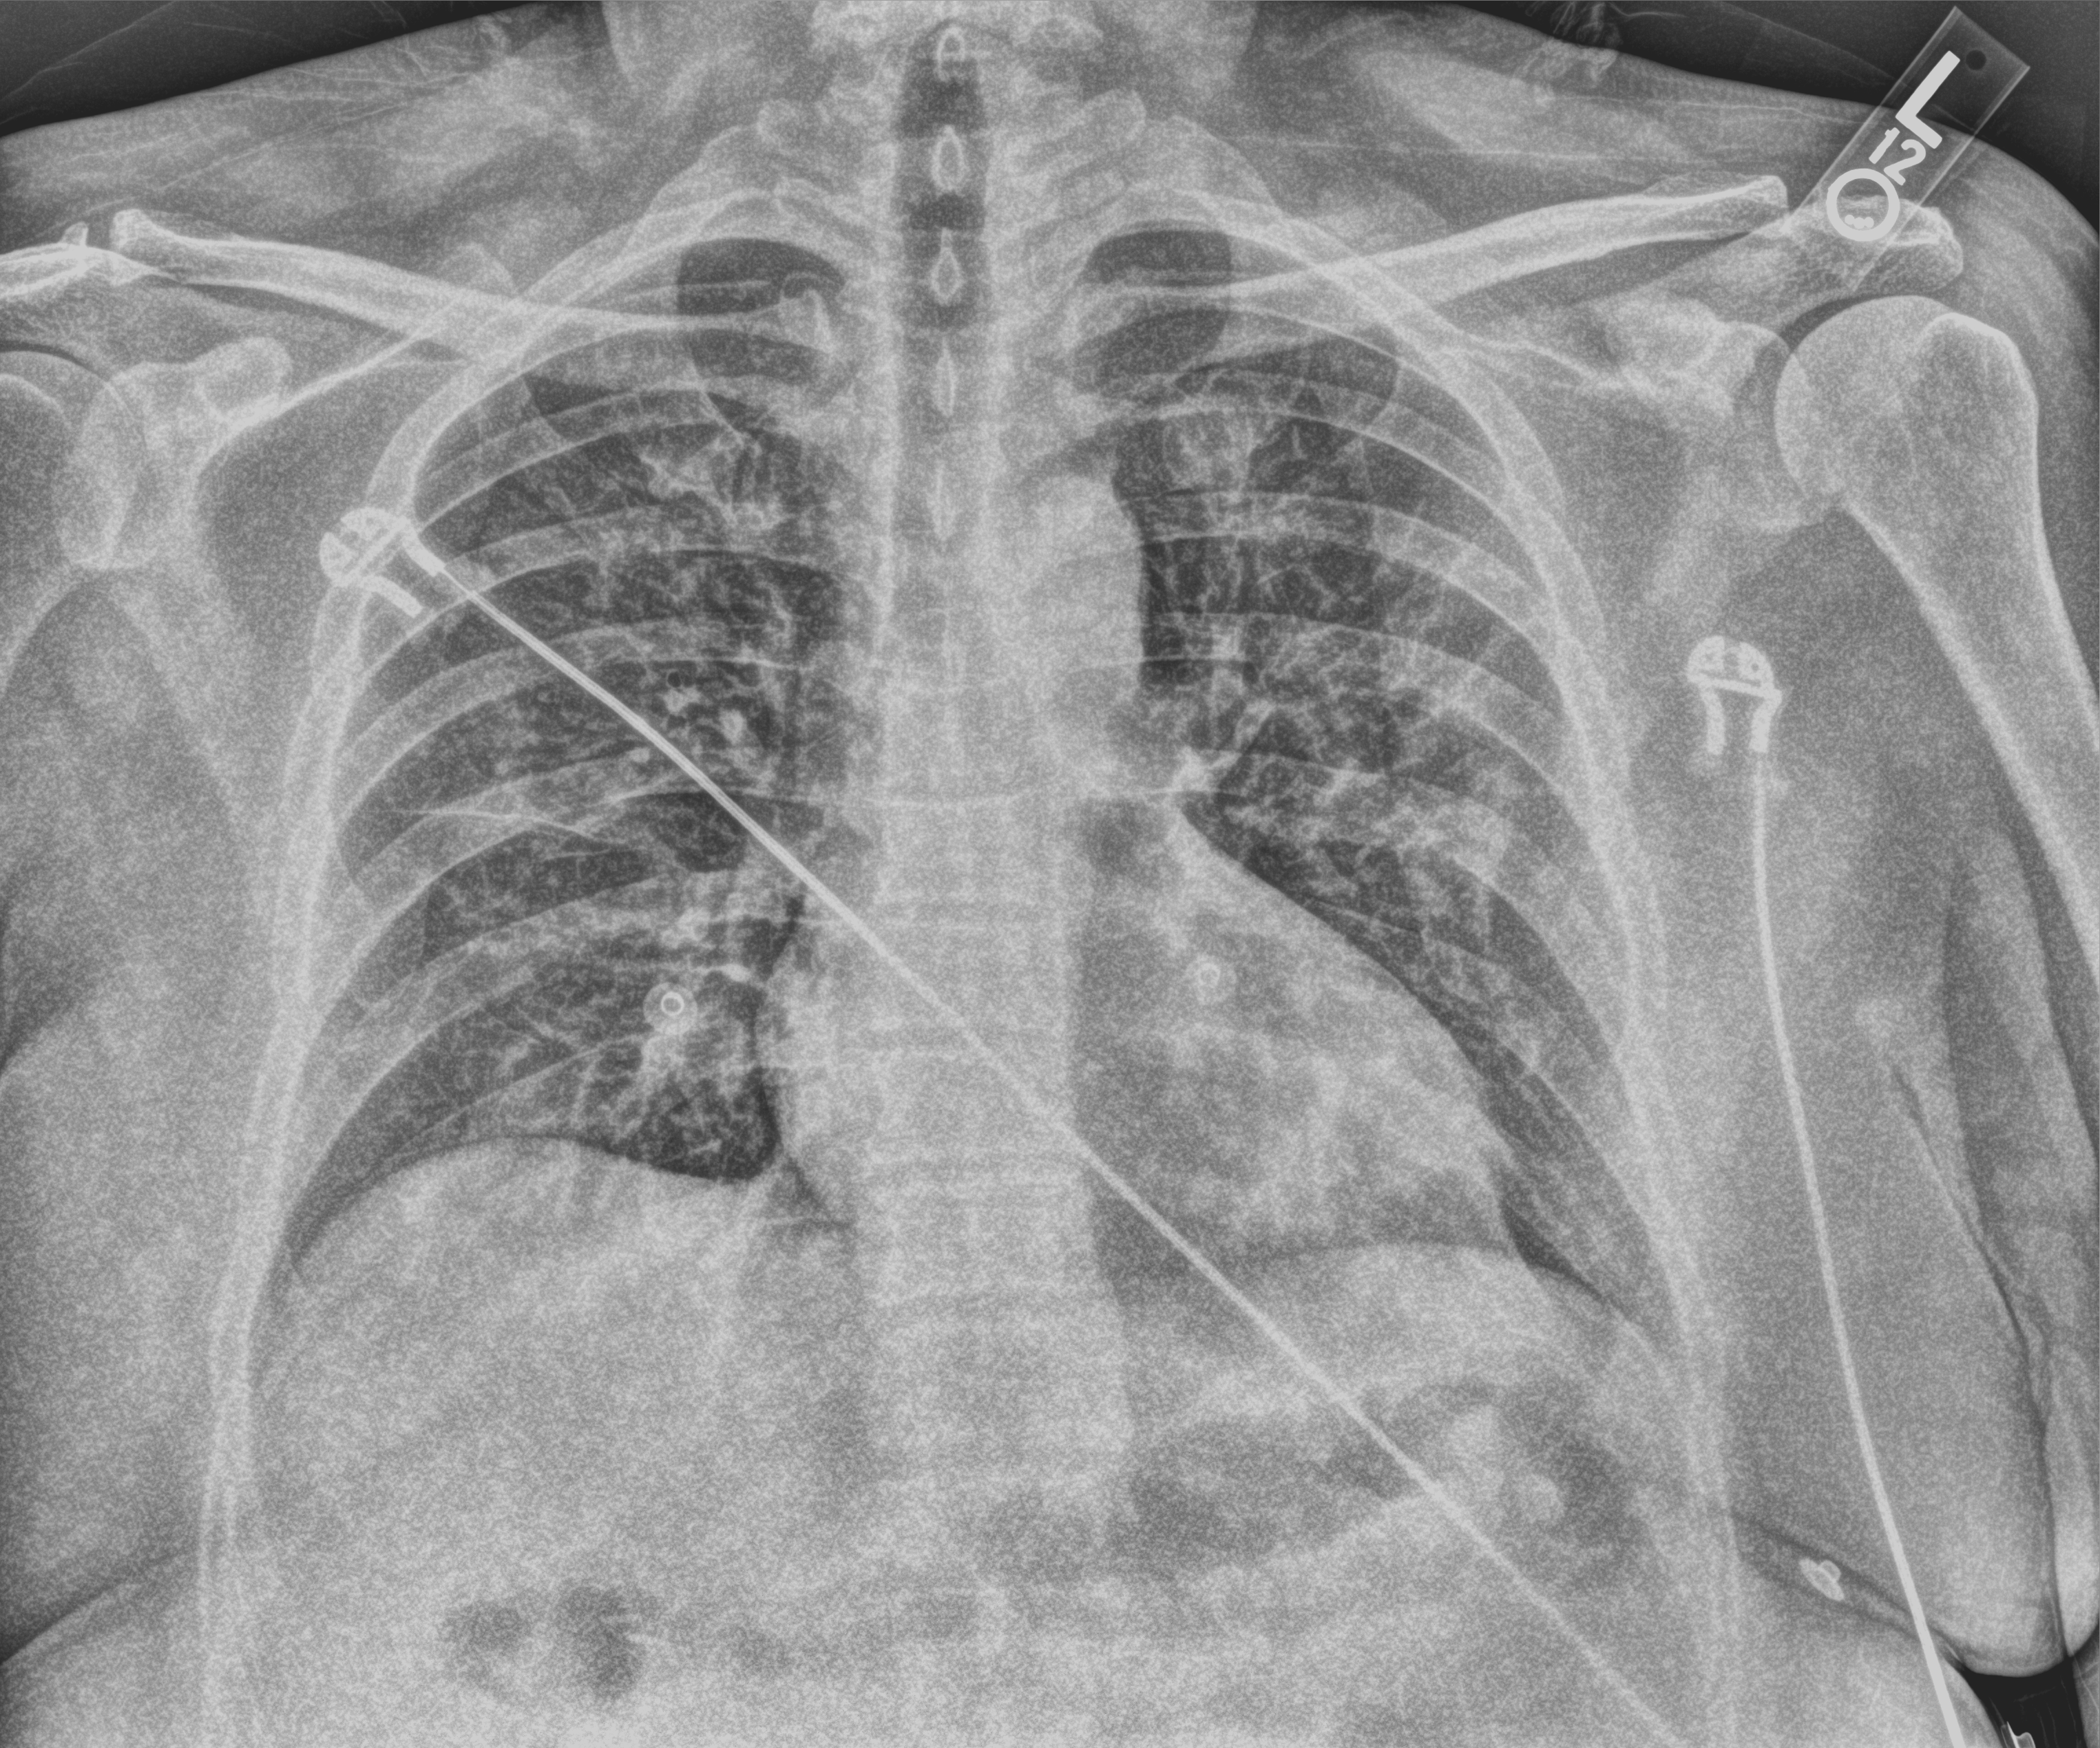
Portable chest radiograph; anteroposterior (AP) projection. Male patient hospitalised with COVID-19, age 60–74 years.
Hospital-stay facts (about this admission, not read from this image; timing relative to this image not recorded):
- admitted to intensive care during this hospital stay: no
- mechanically ventilated during this hospital stay: no